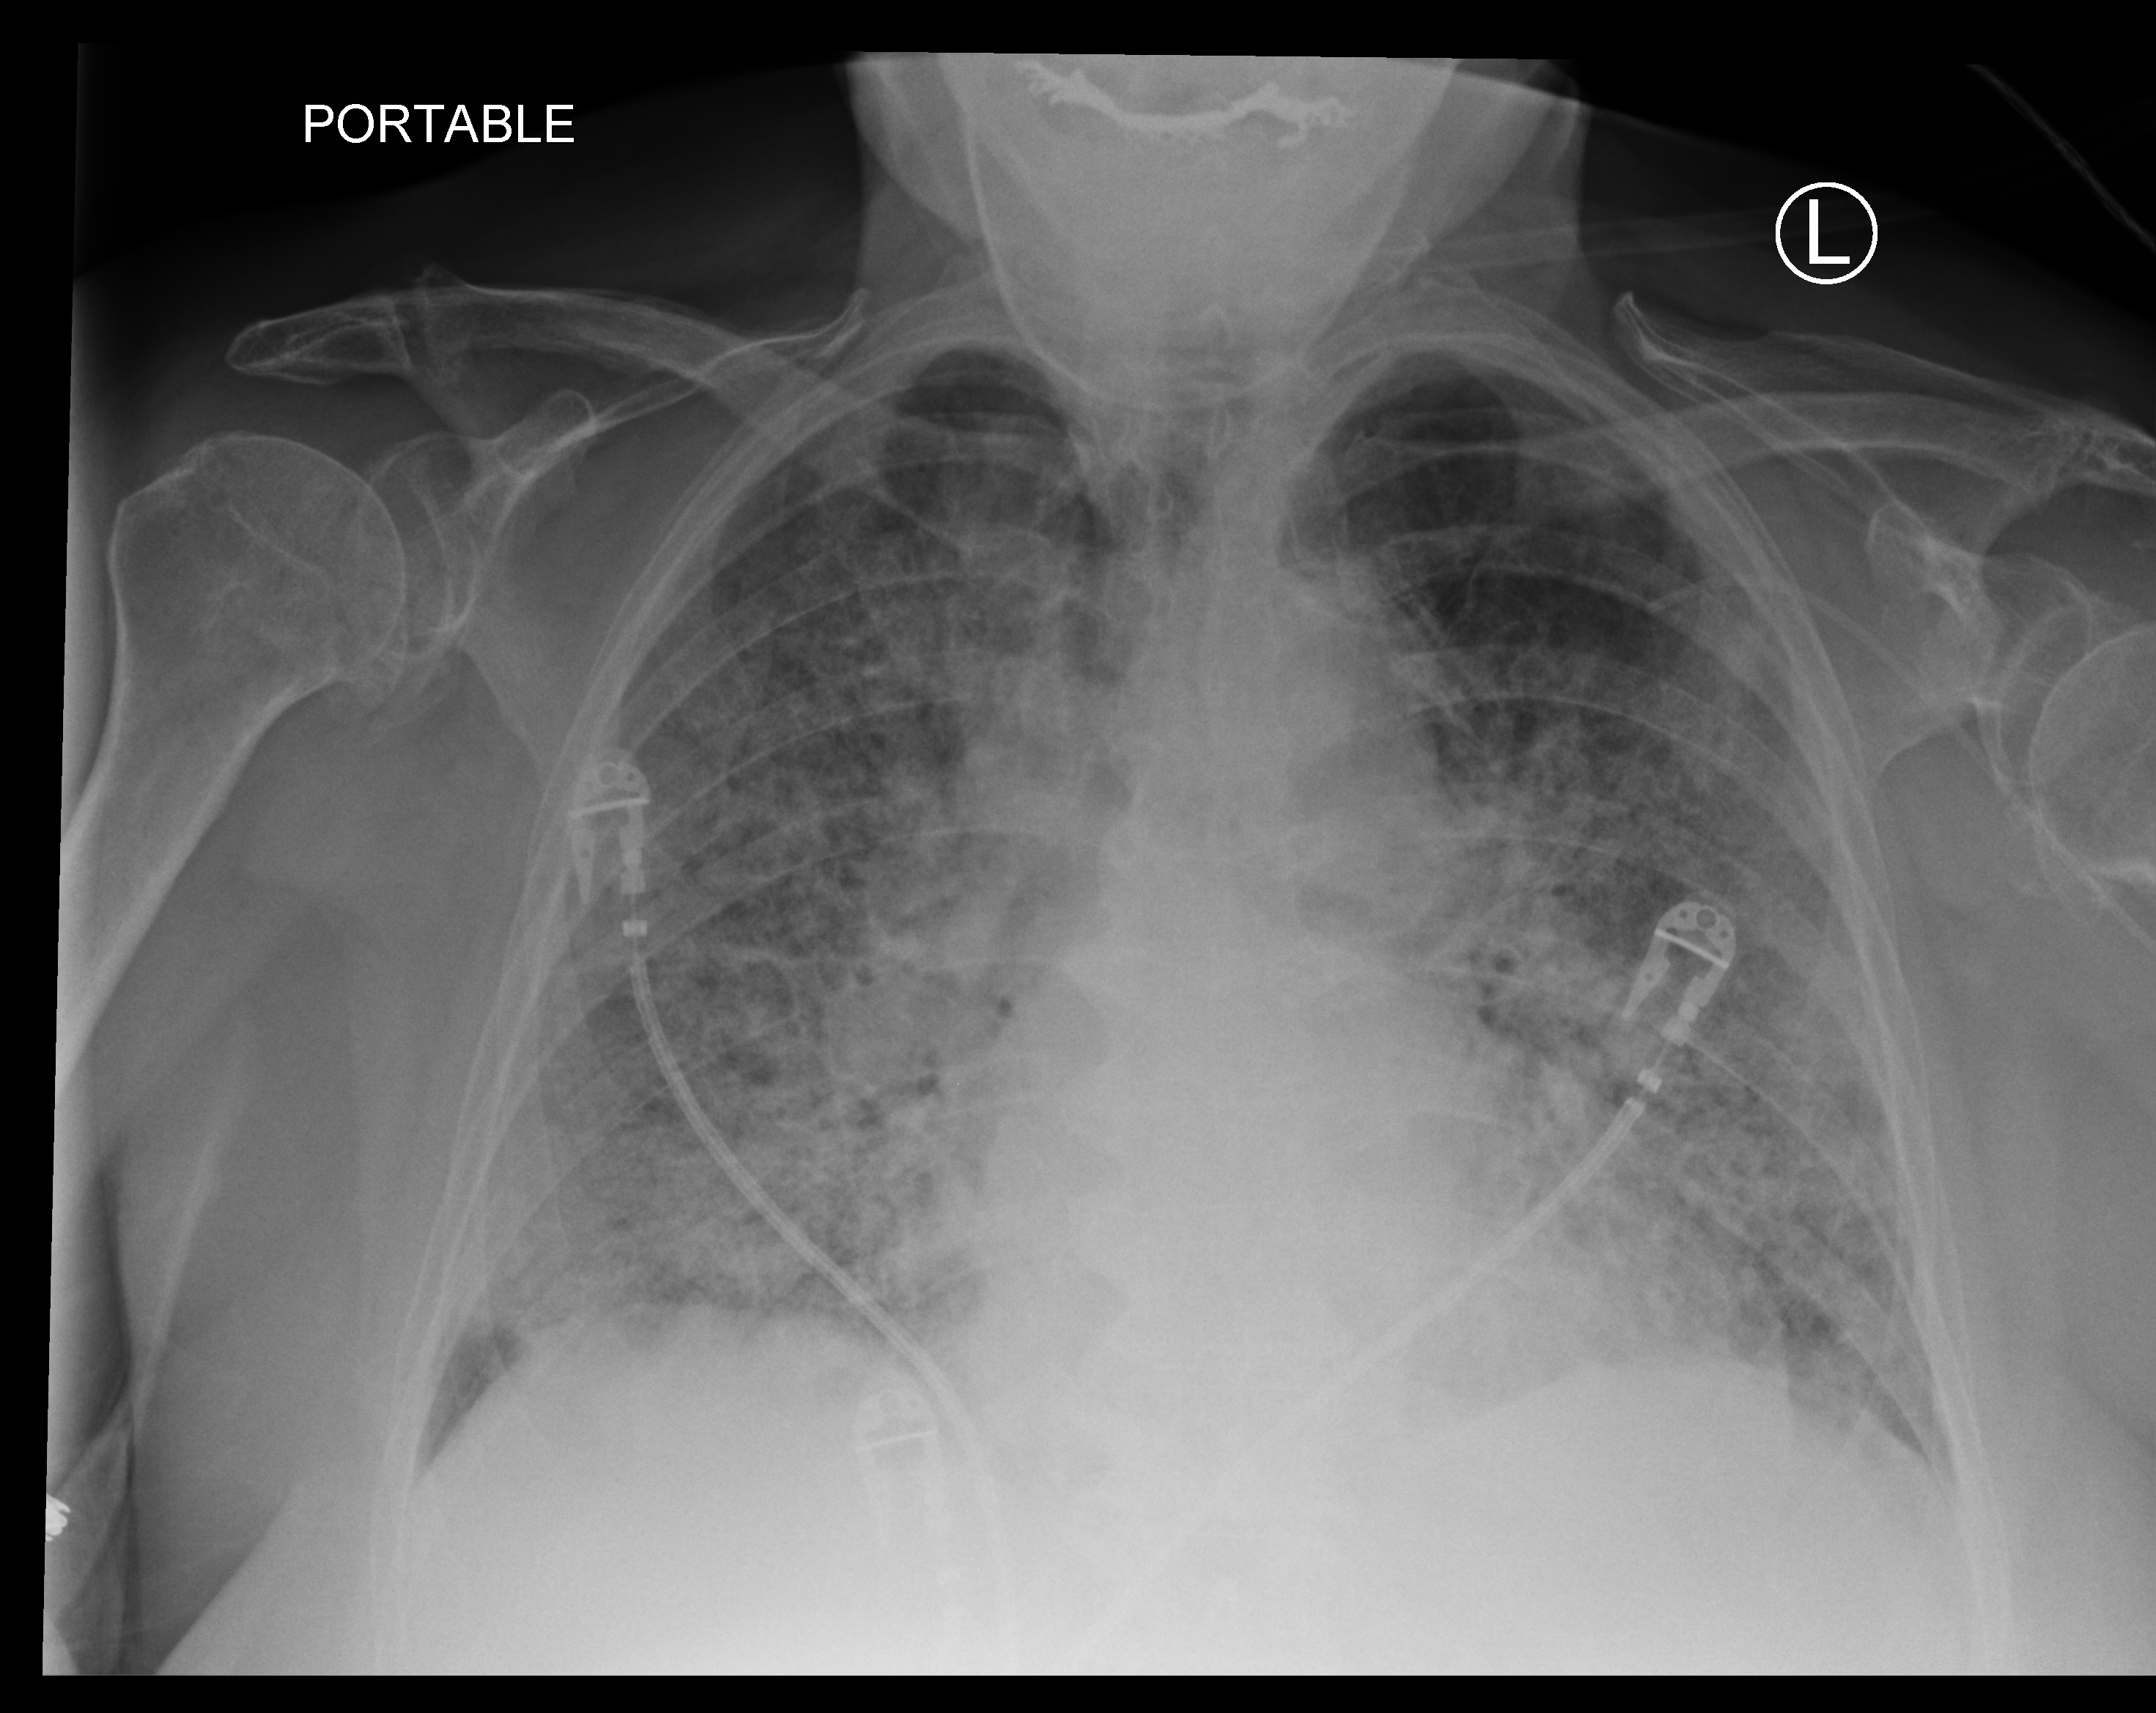
Portable chest radiograph, anteroposterior (AP) projection. Female patient hospitalised with COVID-19, age 75–90 years.
Hospital-stay facts (about this admission, not read from this image; timing relative to this image not recorded): chronic kidney disease (admission record): no; admitted to intensive care during this hospital stay: no; mechanically ventilated during this hospital stay: yes.